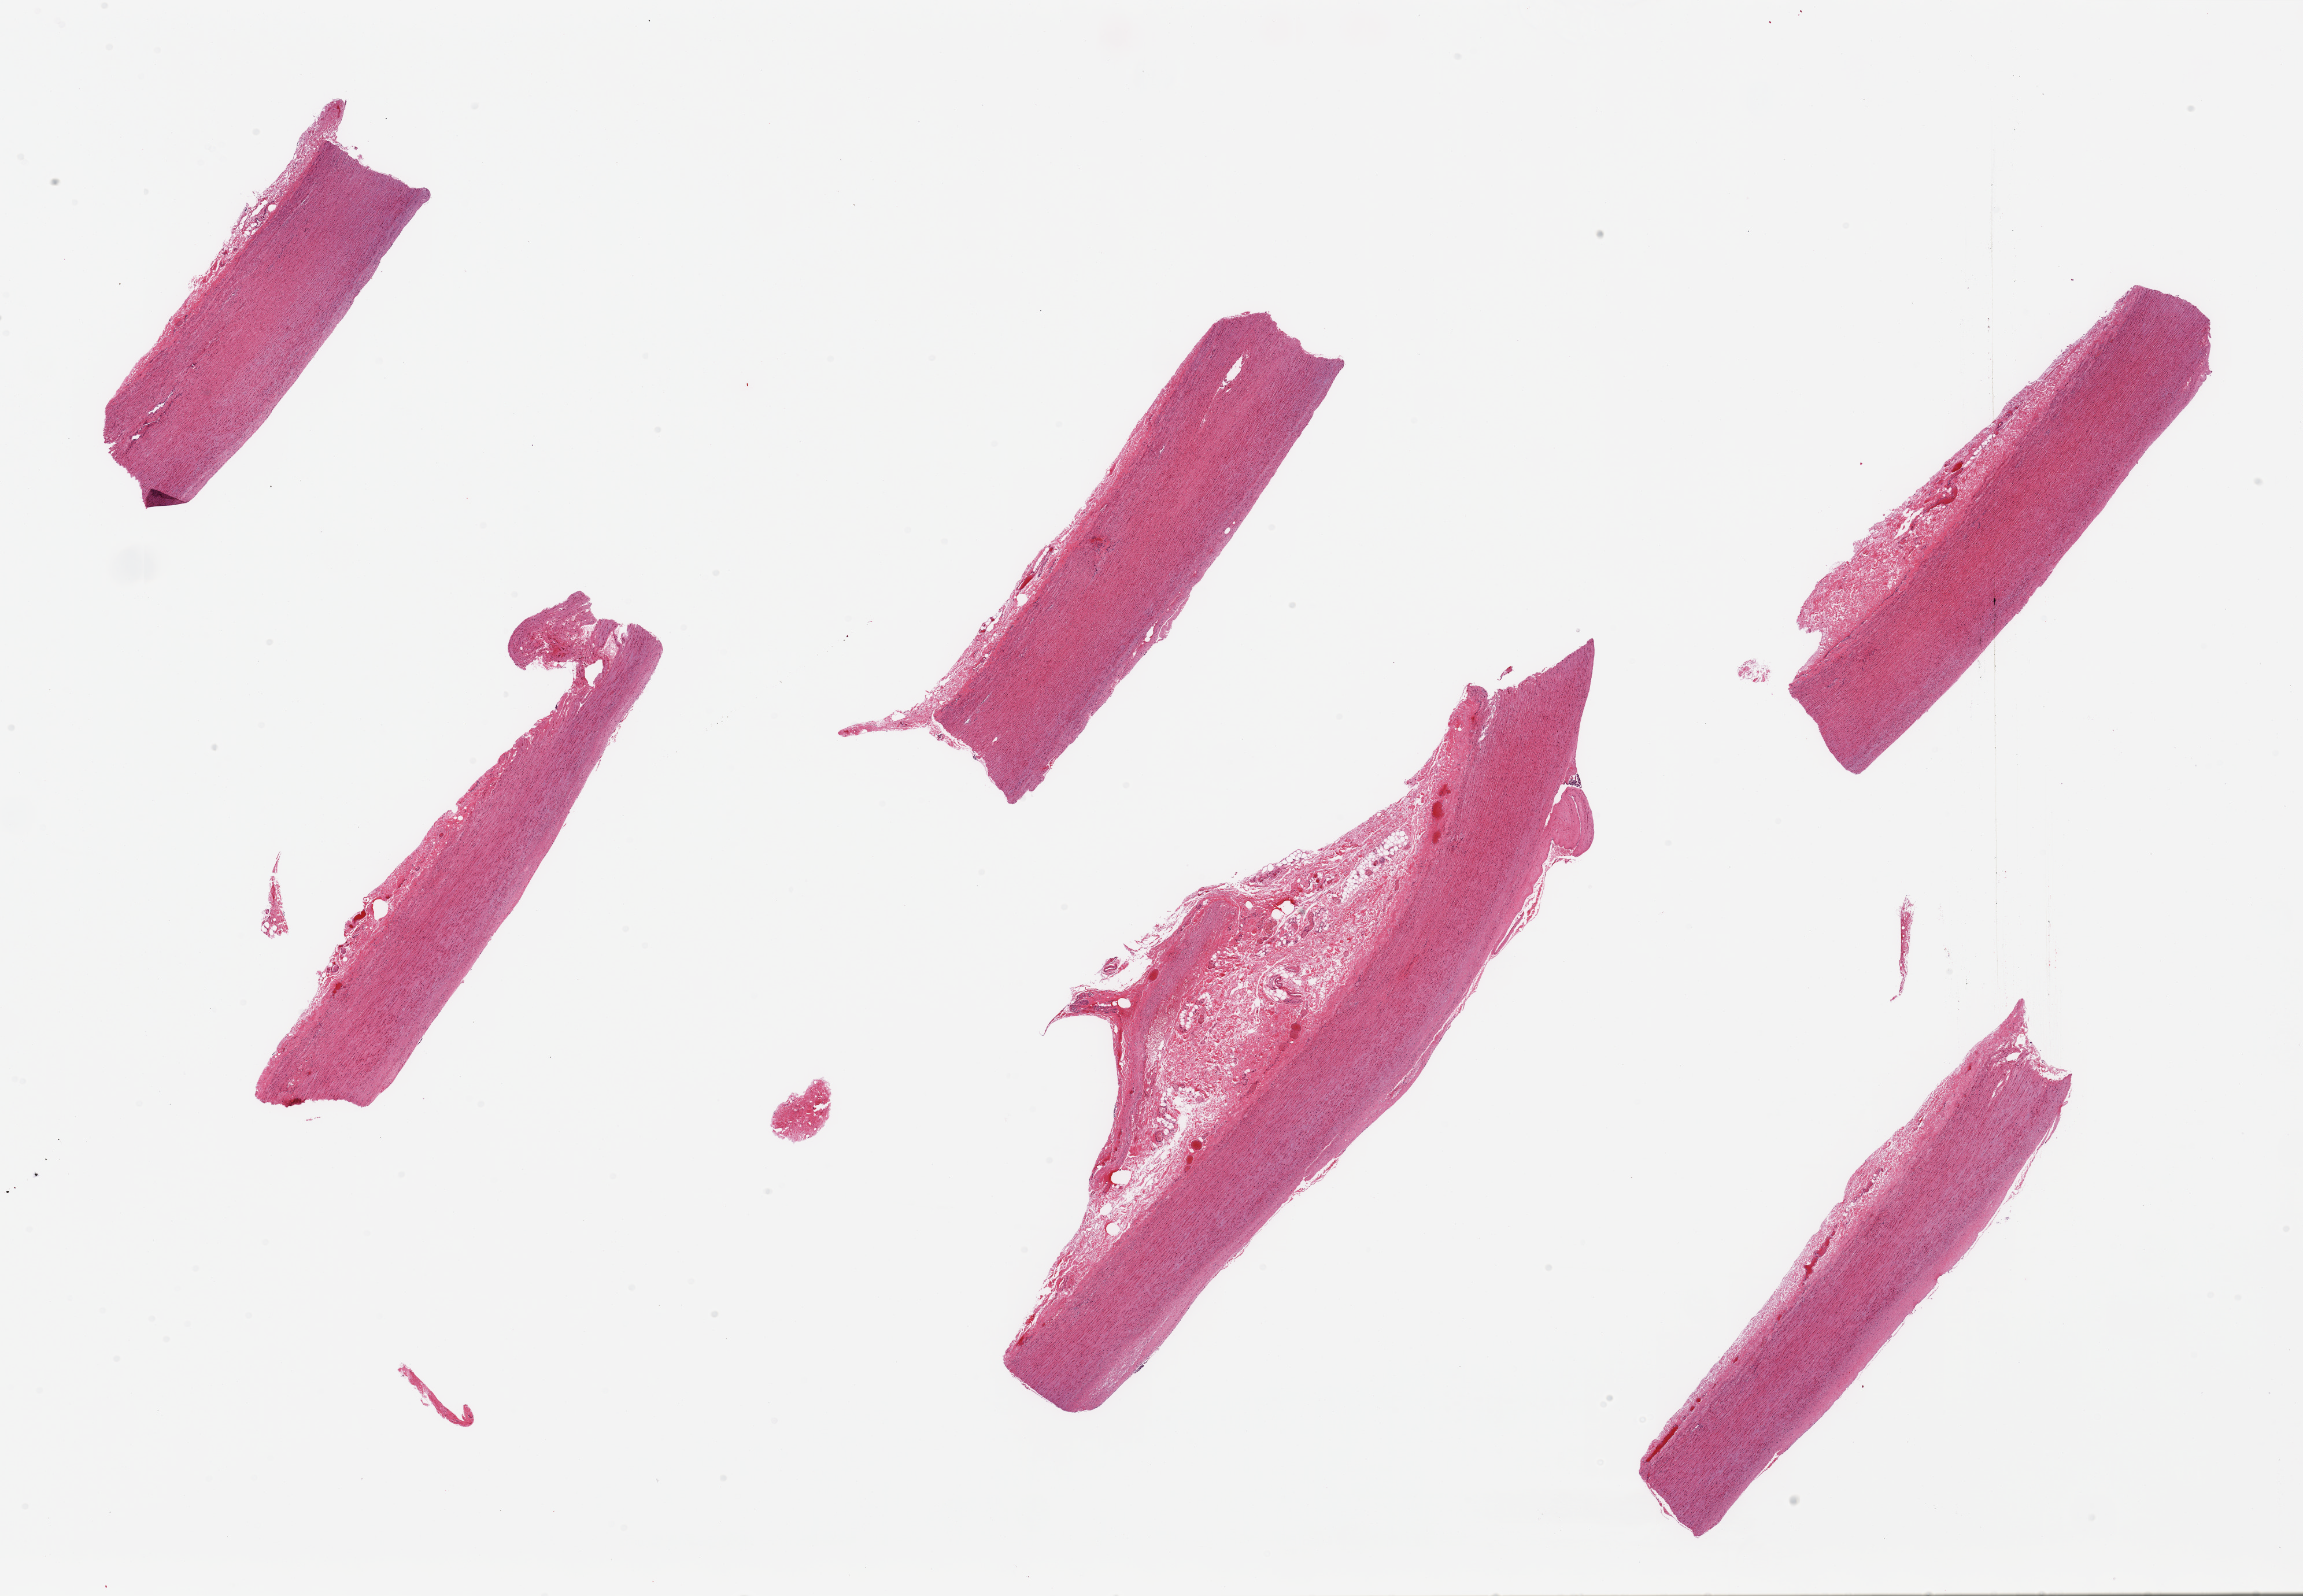
Digitized H&E-stained section, a low-resolution overview of the entire scanned area, about 31.5 x 21.8 mm, PAXgene-fixed paraffin-embedded (PFPE) section, section of aorta (target tissue), tissue donor sample.
Pathologist's review note for this sample: 6 pieces; mild to moderate plaque.